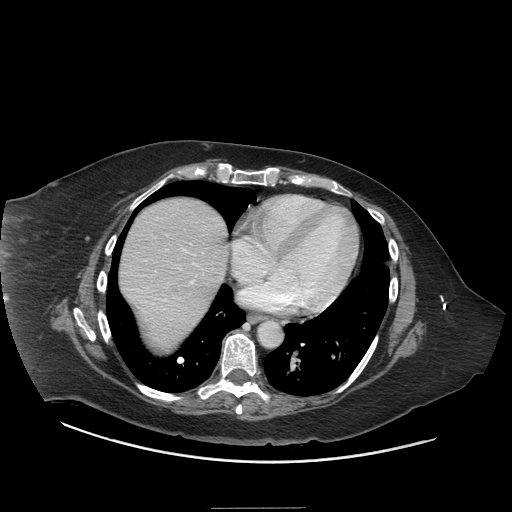
Contrast-enhanced abdominal CT (liver protocol), one axial slice; slice 68 of 81 in the series (ordered by position); 140 kVp; soft-tissue window (W 400 / L 40 HU); 512 × 512 image matrix, field of view 440 × 440 mm. Case-level facts recorded for this patient, not image findings: diagnosis: hepatocellular carcinoma (patient treated with transarterial chemoembolisation; whether this scan precedes or follows treatment is not stated here); TNM stage (as recorded): Stage-II; Child-Pugh class: A.
Annotated regions visible in this slice (semi-automatic segmentation, software-assisted and operator-edited):
- abdominal aorta: bounding box (x1, y1, x2, y2) in pixels: (258, 320, 282, 347)
- liver parenchyma outside the tumour (the mass and vessels are separate outlines, so this box may not span the whole liver): (120, 198, 228, 350)
- liver vessels: (124, 218, 214, 320)